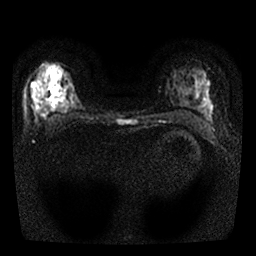
Breast MRI, one axial slice. Slice 17 of 25 in the series (ordered by position). Diffusion-weighted series; image 2 of 4 stored at this slice position (different b-values; order by instance number). 1.5 T. 4 mm slice thickness. 256 × 256 image matrix, field of view 300 × 300 mm. Female patient.
Annotated regions visible in this slice (outlined manually by an expert reader):
- tumour on diffusion-weighted imaging: bounding box (x1, y1, x2, y2) in pixels: (33, 89, 41, 110)